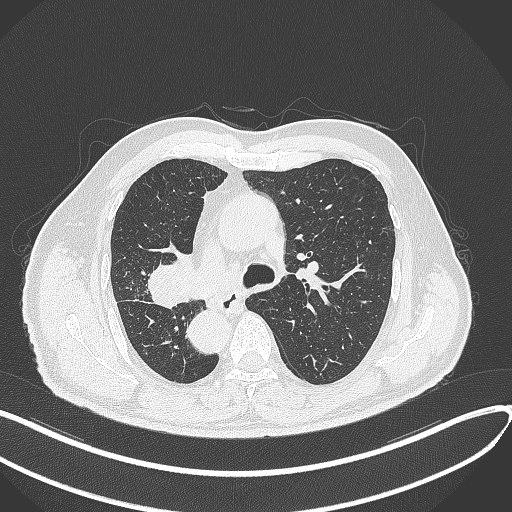
Chest CT, one axial slice; slice 201 of 300 in the series (ordered by position); reconstruction kernel B70f; 120 kVp; lung window (W 1500 / L -600 HU); 1 mm slice thickness; 512 × 512 image matrix, field of view 400 × 400 mm. Patient: male, 67 years. From the clinical record (not read from this slice): clinical TNM (as recorded): T2a N0 M0.
Annotated regions visible in this slice (rectangle marked by the reading radiologist):
- lung tumour (recorded histology: squamous cell carcinoma): bounding box [x1, y1, x2, y2] px = [148, 250, 193, 313]